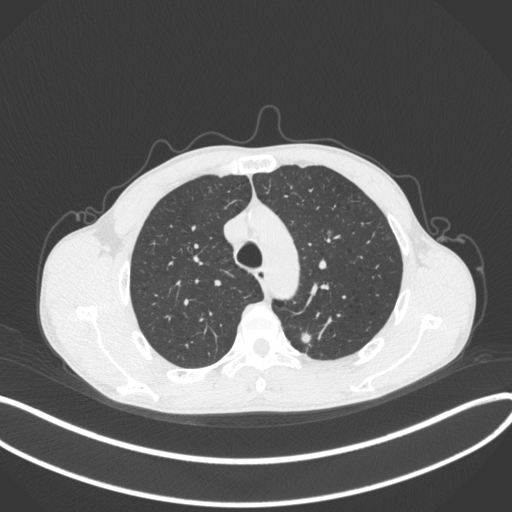
Chest CT, one axial slice. 120 kVp. Lung window (W 1500 / L -600 HU). 512 × 512 image matrix, field of view 400 × 400 mm. Male patient, age 51 years. From the clinical record (not read from this slice): clinical TNM (as recorded): T2a N1 M1.
Structures marked on this image (rectangle marked by the reading radiologist):
- lung tumour (recorded histology: adenocarcinoma): bounding box (x1, y1, x2, y2) in pixels: (295, 328, 312, 348)